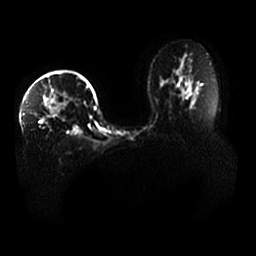
Breast MRI, one axial slice. Slice 28 of 33 in the series (ordered by position). Diffusion-weighted series; image 2 of 4 stored at this slice position (different b-values; order by instance number). 1.5 T. 4 mm slice thickness. 256 × 256 image matrix. Female patient.
Outlined on this slice (manually delineated by an expert):
- tumour on diffusion-weighted imaging: bounding box <42,94,81,122> (left, top, right, bottom; pixels)